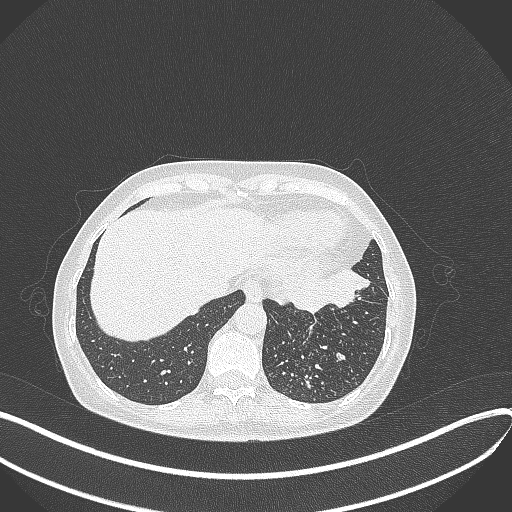
Chest CT, one axial slice. Slice 88 of 429 in the series (ordered by position). Reconstruction kernel B70f. 100 kVp. Lung window (W 1500 / L -600 HU). 1 mm slice thickness. 512 × 512 image matrix, field of view 400 × 400 mm. Female patient, age 63 years. From the clinical record (not read from this slice): clinical TNM (as recorded): T1b N0 M0; histopathological grade: G2-3.
Annotated regions visible in this slice (bounding box drawn by a radiologist):
- lung tumour (recorded histology: adenocarcinoma): box from (x=282, y=265) to (x=371, y=313) px